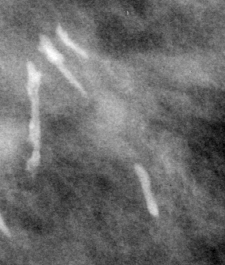
Region of interest cut from a scanned film mammogram (one marked finding); left breast; MLO view; BI-RADS breast density category 3 (scale 1–4).
- Marked abnormality: calcifications, morphology large rodlike / round and regular, distribution regional; BI-RADS assessment category 2; subtlety rating 5 on a 1 (subtle) to 5 (obvious) scale; benign; no additional work-up was recommended (benign without callback).